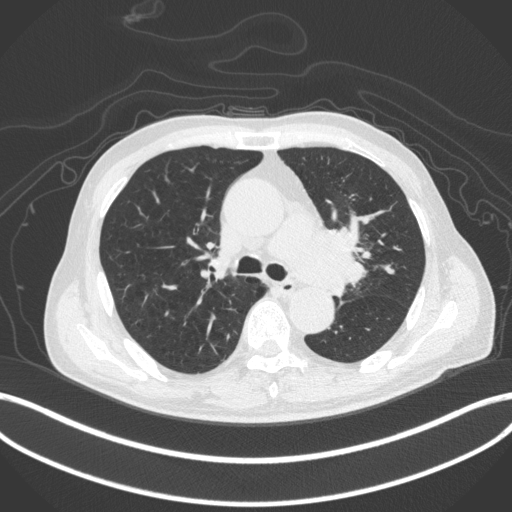
Chest CT, one axial slice; slice 280 of 420 in the series (ordered by position); reconstruction kernel B31f; lung window (W 1500 / L -600 HU); 512 × 512 image matrix, field of view 400 × 400 mm. Male patient, age 77 years. Case-level facts recorded for this patient, not image findings: clinical TNM (as recorded): T3 N1 M0.
Outlined on this slice (rectangle marked by the reading radiologist):
- lung tumour (recorded histology: adenocarcinoma): bounding box (x1, y1, x2, y2) in pixels: (306, 224, 368, 294)